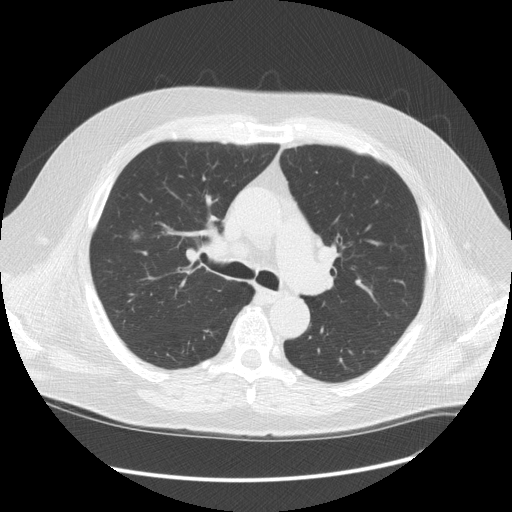
Low-dose screening chest CT, one axial slice. Reconstruction kernel STANDARD. 120 kVp. Lung window (W 1500 / L -600 HU). 2.5 mm slice thickness. 512 × 512 image matrix, field of view 401 × 401 mm.
Outlined on this slice (outlined manually by an expert reader):
- lesion 1 (tumor, upper lobe of right lung): bounding box [x1, y1, x2, y2] px = [133, 232, 139, 239]